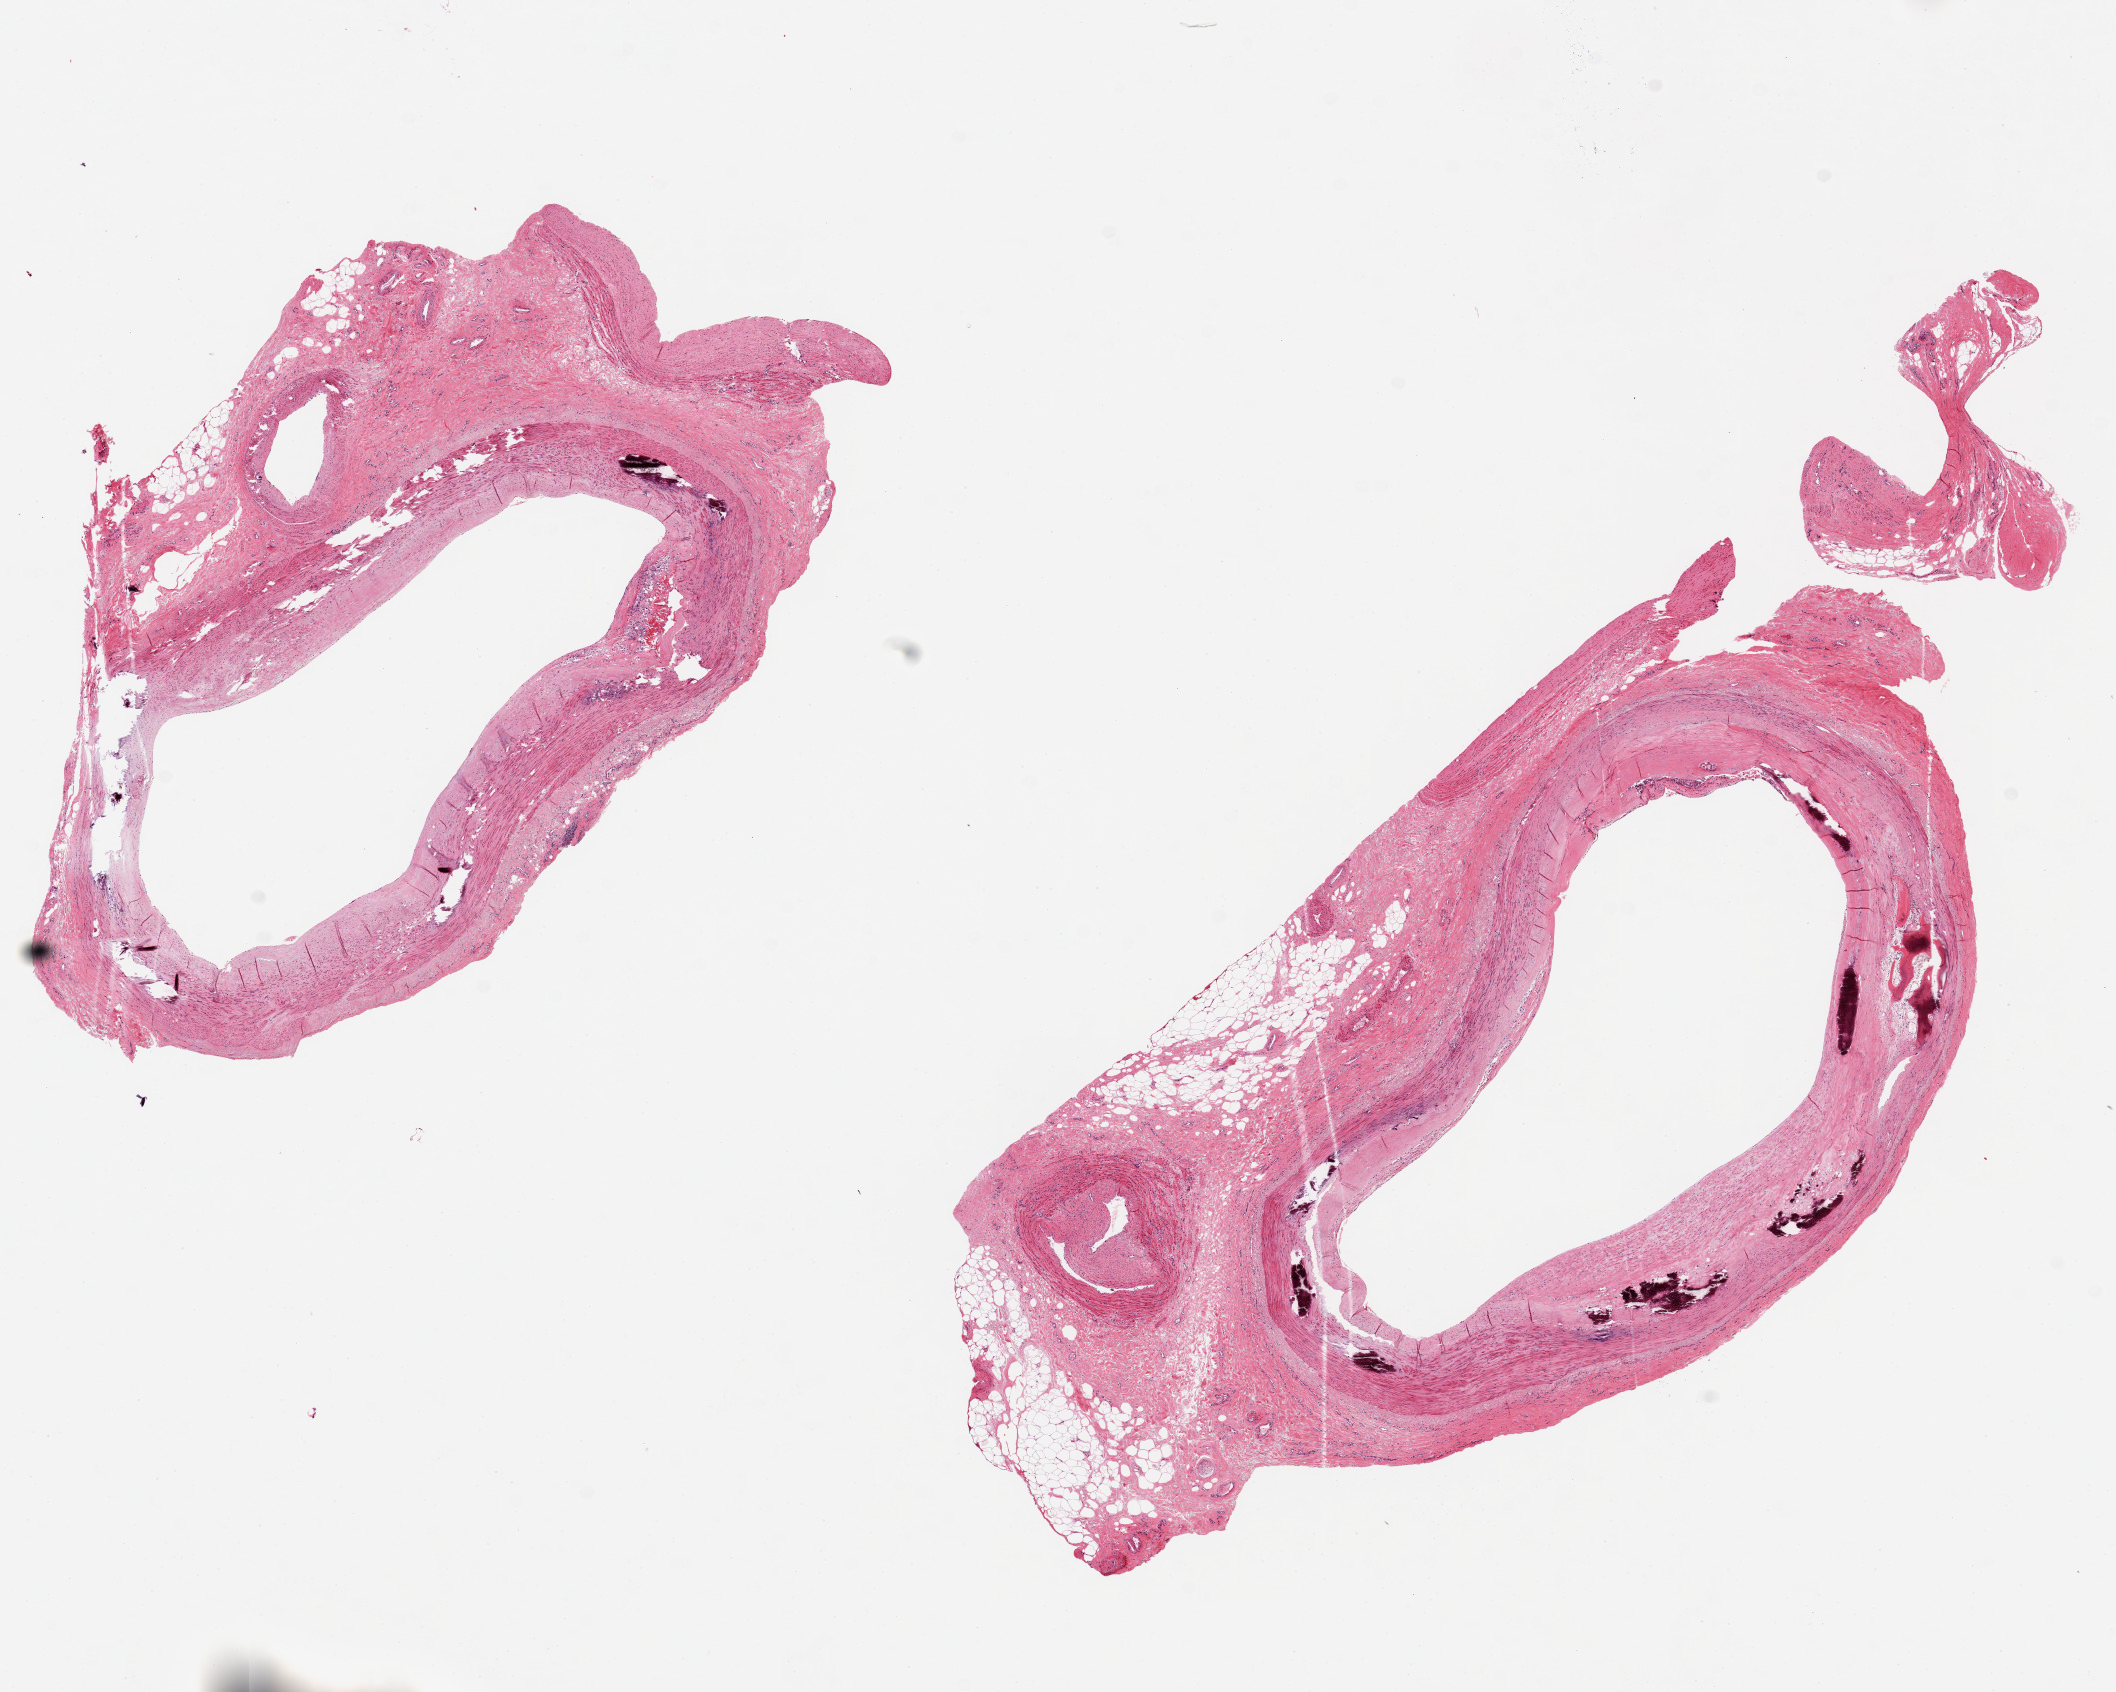
Whole-slide image, hematoxylin and eosin (H&E) stain — low-resolution overview of the scanned area, about 16.7 x 13.4 mm. PAXgene-fixed paraffin-embedded (PFPE) section. Section of tibial artery (target tissue). Tissue donor sample. Male donor.
Review note (as recorded): 2 pieces ~6x4mm; Arteries, adherent fibroadipose tissue present on both, ~30% of both.